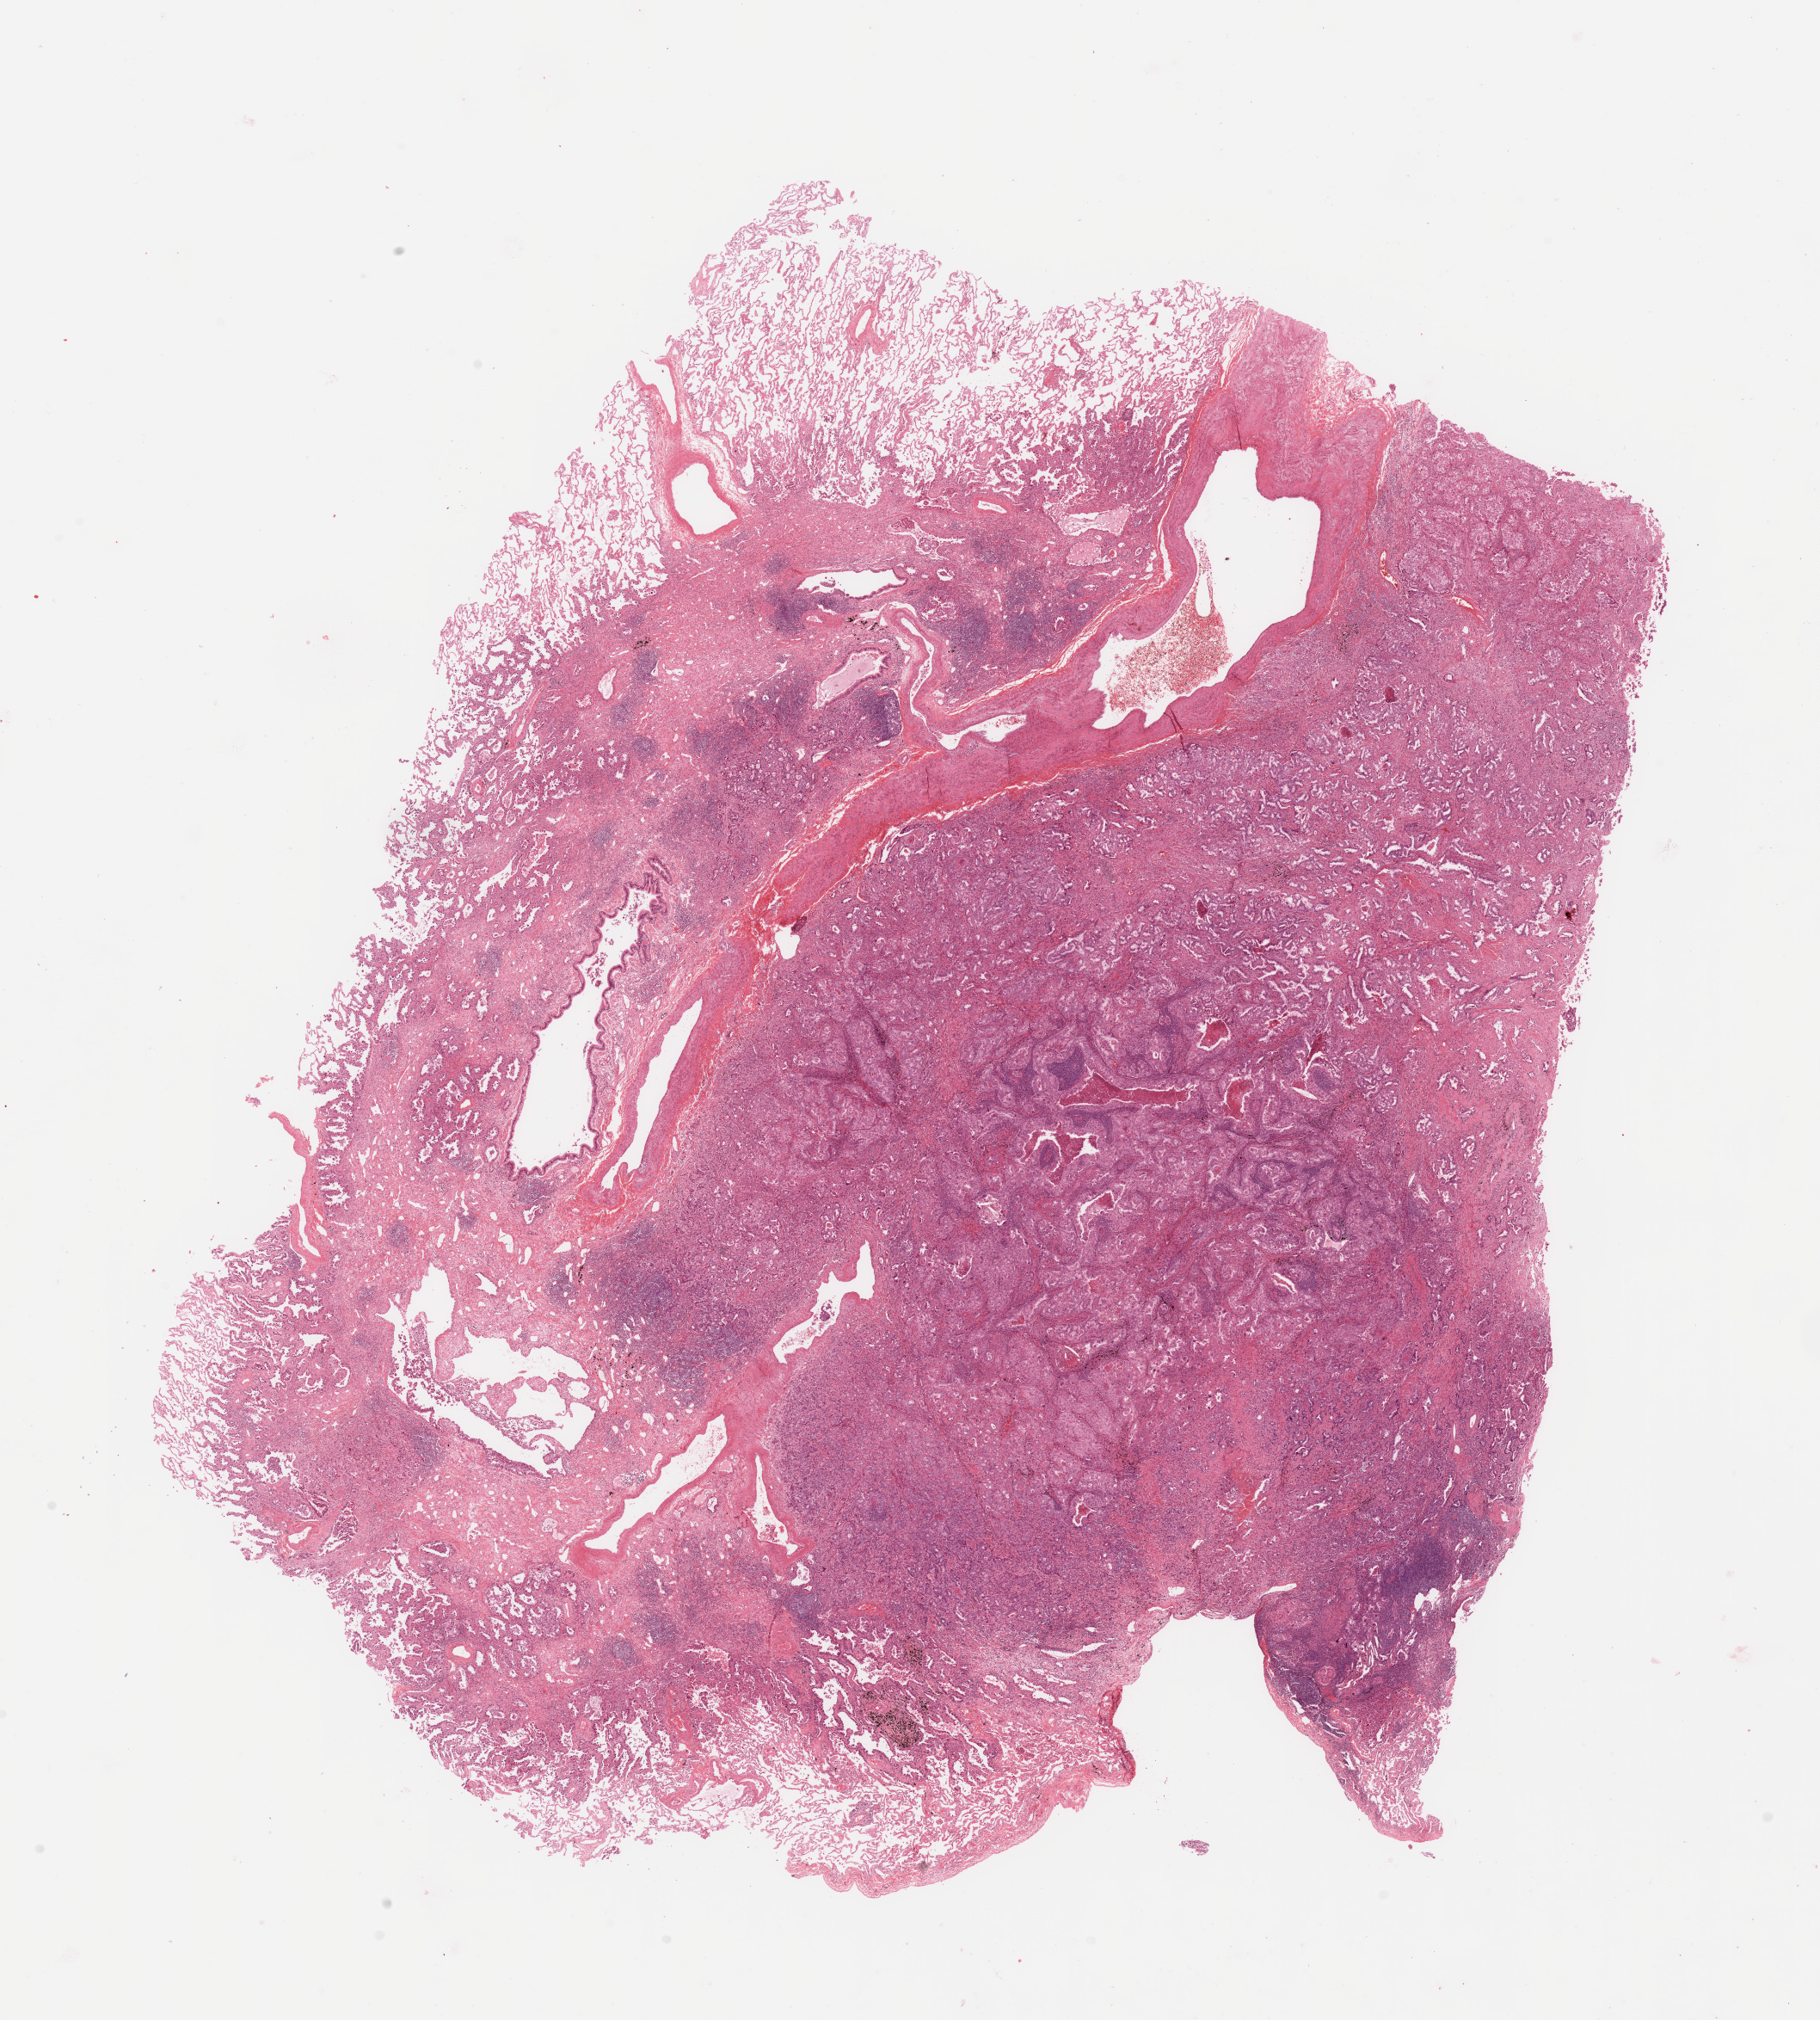
Whole-slide histology image, Hematoxylin and eosin (H&E) stained, shown as a low-resolution overview of the whole scanned area (about 16.7 x 18.6 mm, from a 20x scan). Tumour tissue sample, lung. Female, 62 y/o. Histologic grade: G3 (poorly differentiated).
Histologic diagnosis: Adenocarcinoma, NOS. AJCC pathologic stage: IB. Primary tumour site (as recorded): left upper lobe.